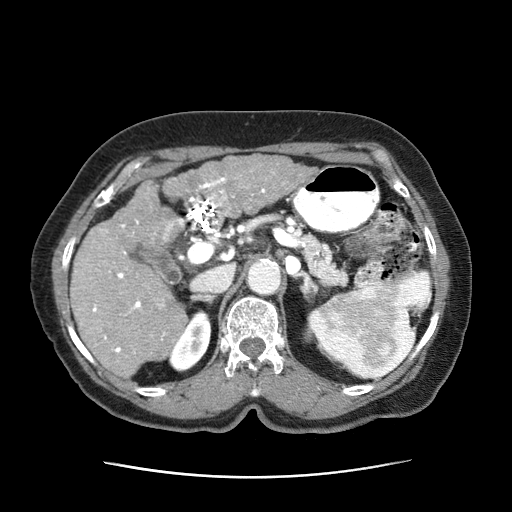
Contrast-enhanced abdominal CT (liver protocol), one axial slice. Position 32 of 63 along the scan axis. Reconstruction kernel STANDARD. 120 kVp. Intravenous contrast given. Soft-tissue window (W 400 / L 40 HU). 2.5 mm slice thickness. 512 × 512 image matrix, field of view 360 × 360 mm. Patient: female, 79 years. Case-level facts recorded for this patient, not image findings: diagnosis: hepatocellular carcinoma (patient treated with transarterial chemoembolisation; whether this scan precedes or follows treatment is not stated here); TNM stage (as recorded): Stage-II; Child-Pugh class: B; tumour differentiation: well differentiated; tumour nodularity: multinodular.
Annotated regions visible in this slice (semi-automatically segmented with operator editing):
- abdominal aorta: box from (x=247, y=258) to (x=281, y=295) px
- liver parenchyma outside the tumour (the mass and vessels are separate outlines, so this box may not span the whole liver): (x=70, y=179)–(x=187, y=380)
- mass: (x=164, y=154)–(x=317, y=214)
- liver vessels: (x=92, y=177)–(x=235, y=354)